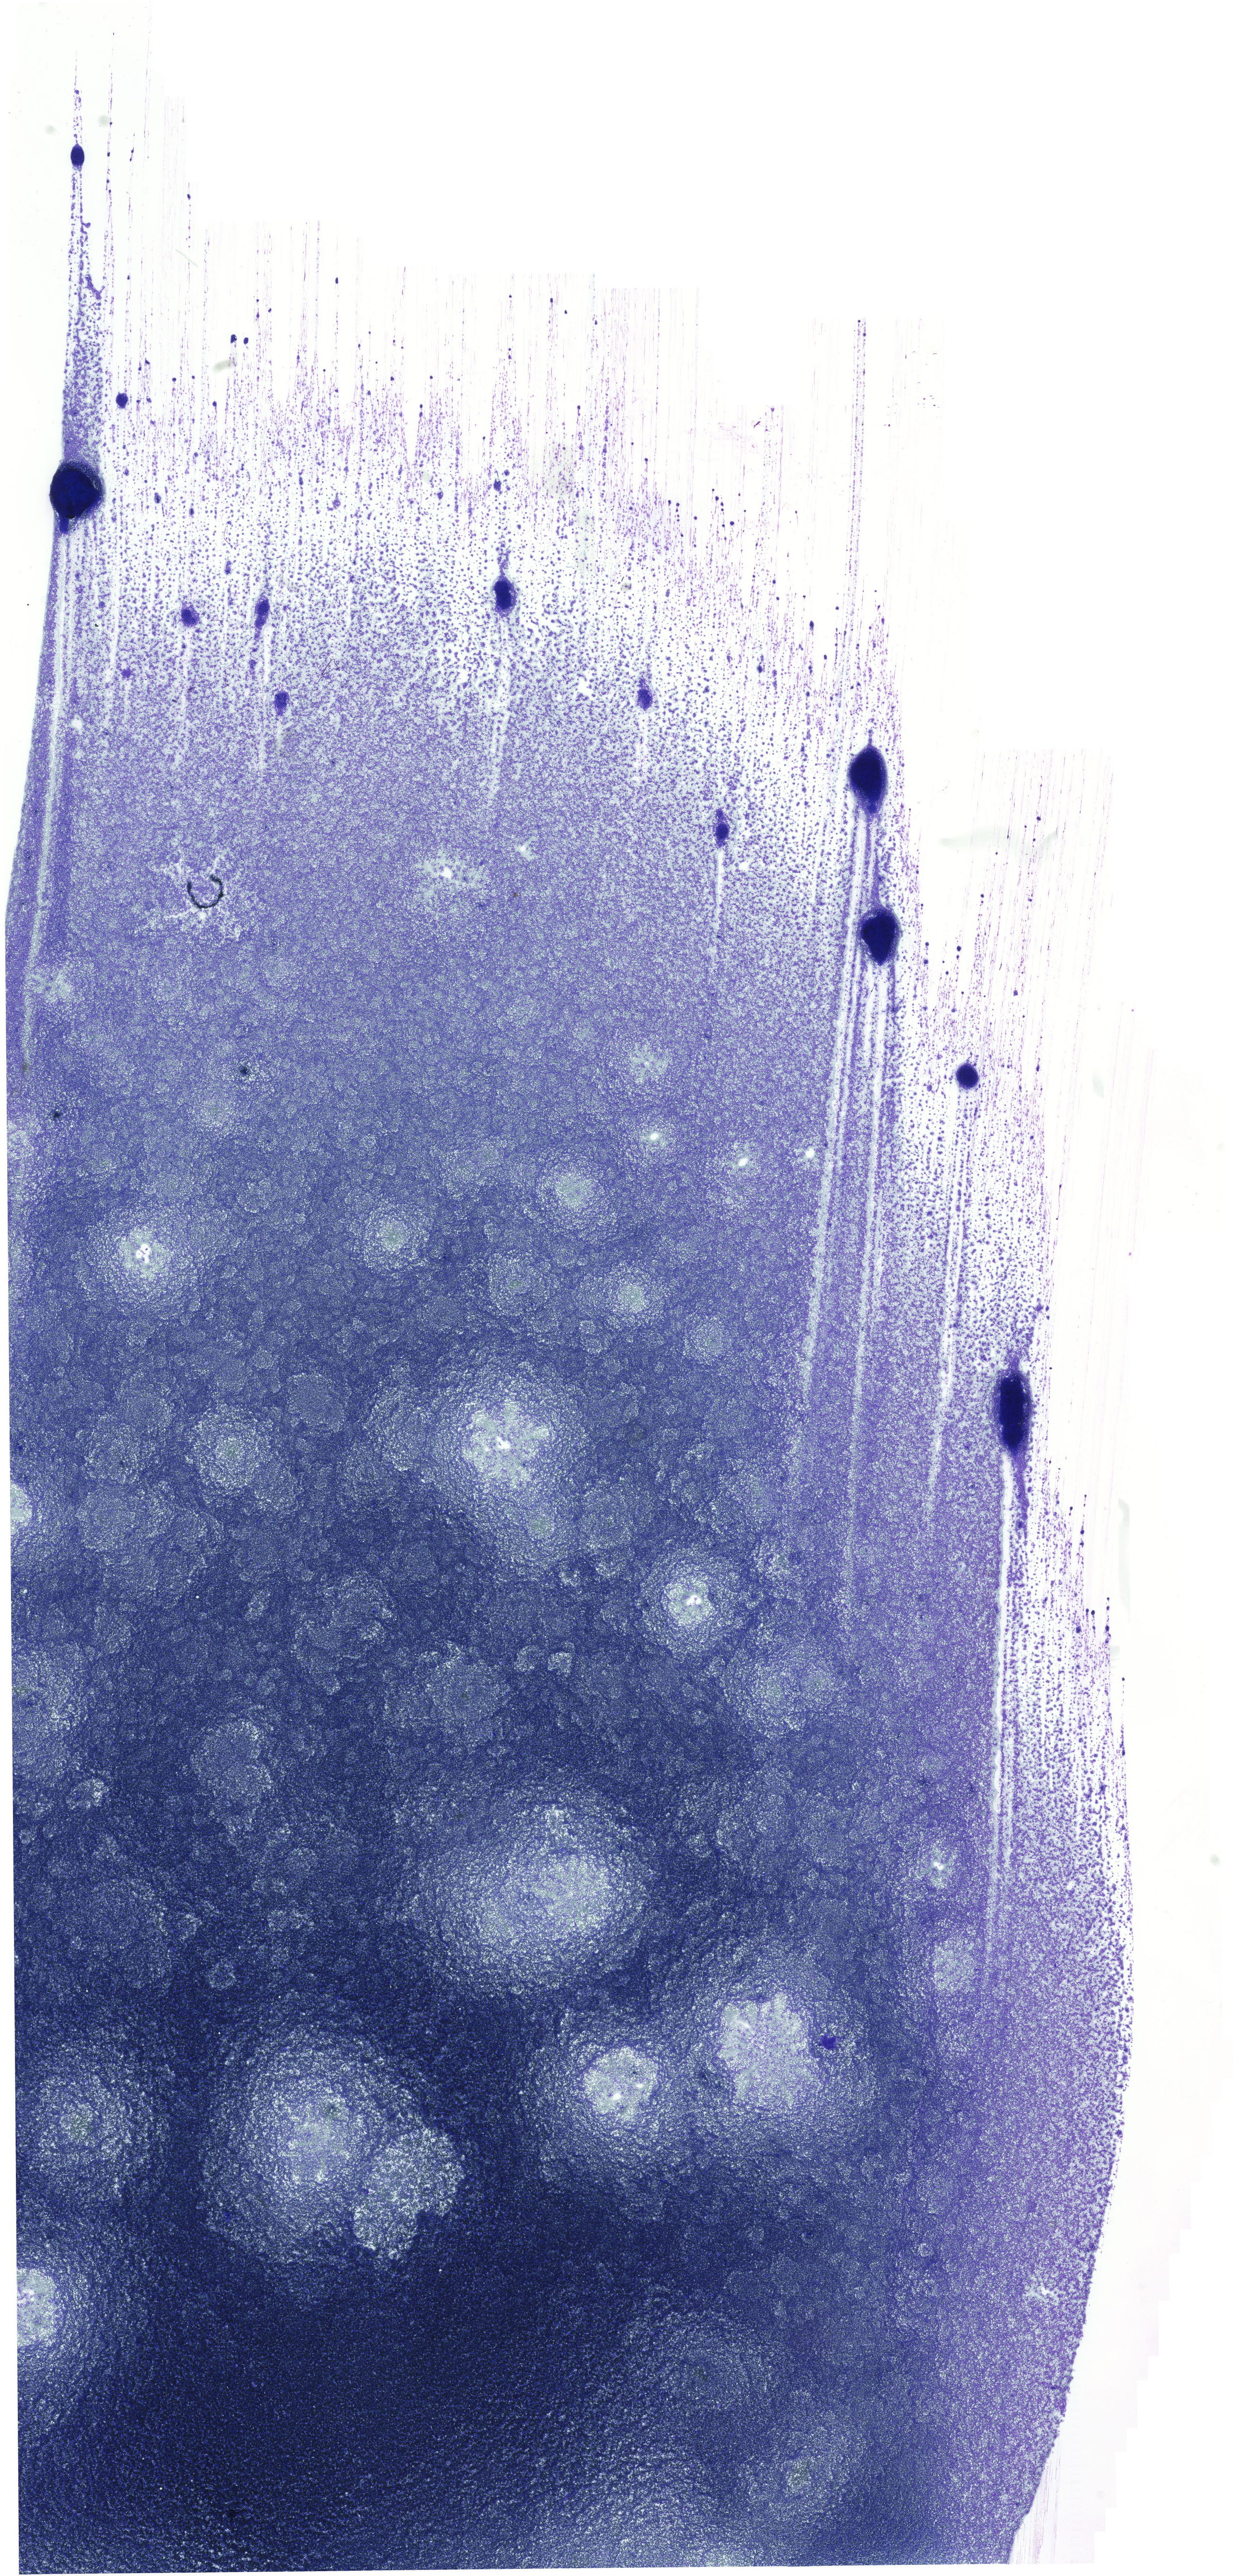
Bone marrow aspirate smear, May-Grünwald-Giemsa (MGG) stain, whole-slide image — low-resolution overview of the scanned area, about 18.2 x 37.9 mm. Patient sex: male.
Diagnosis: Chronic Phase Chronic Myeloid Leukemia, BCR-ABL1 Positive.